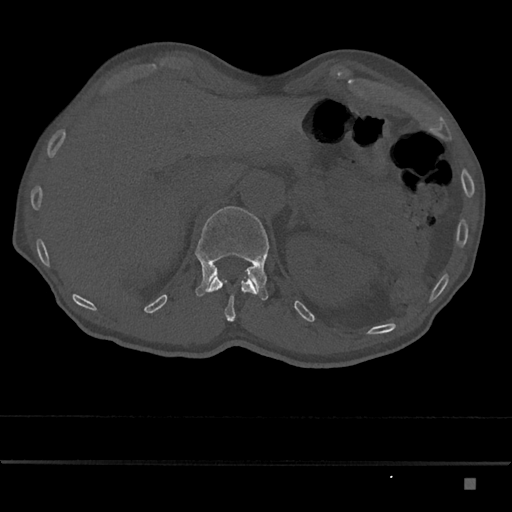
CT including the spine, one axial slice. Position 575 of 797 along the scan axis. Reconstruction kernel Br40s/3. 120 kVp. Bone window (W 1800 / L 400 HU). 0.5 mm slice thickness. 512 × 512 image matrix, field of view 390 × 390 mm. Male patient, age 72 years. From the clinical record (not read from this slice): primary cancer: prostate.
Annotated regions visible in this slice (semi-automatically segmented with operator editing):
- L1 vertebra: bounding box [x1, y1, x2, y2] px = [195, 206, 270, 301]
- T12 vertebra: [206, 275, 256, 322]